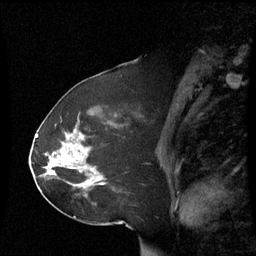
Breast MRI (dynamic contrast-enhanced), one sagittal slice; slice 35 of 60 in the series (ordered by position); dynamic contrast-enhanced series, image 2 of 3 at this slice position (ordered by acquisition); 1.5 T; TE 4.2 ms, TR 8.9 ms; 256 × 256 image matrix, field of view 230 × 230 mm. Female patient, age 51 years. From the clinical record (not read from this slice): setting: breast cancer imaged before/during neoadjuvant chemotherapy; receptor status: HR-positive, HER2-negative.
Structures marked on this image (semi-automatic segmentation, software-assisted and operator-edited):
- analysis volume of interest (the breast-tissue region the enhancement analysis was run in; not a lesion): bounding box [x1, y1, x2, y2] px = [42, 121, 113, 199]
- tumour enhancement mask (voxels above the 70 % enhancement threshold inside the analysis volume of interest): [94, 172, 103, 184]